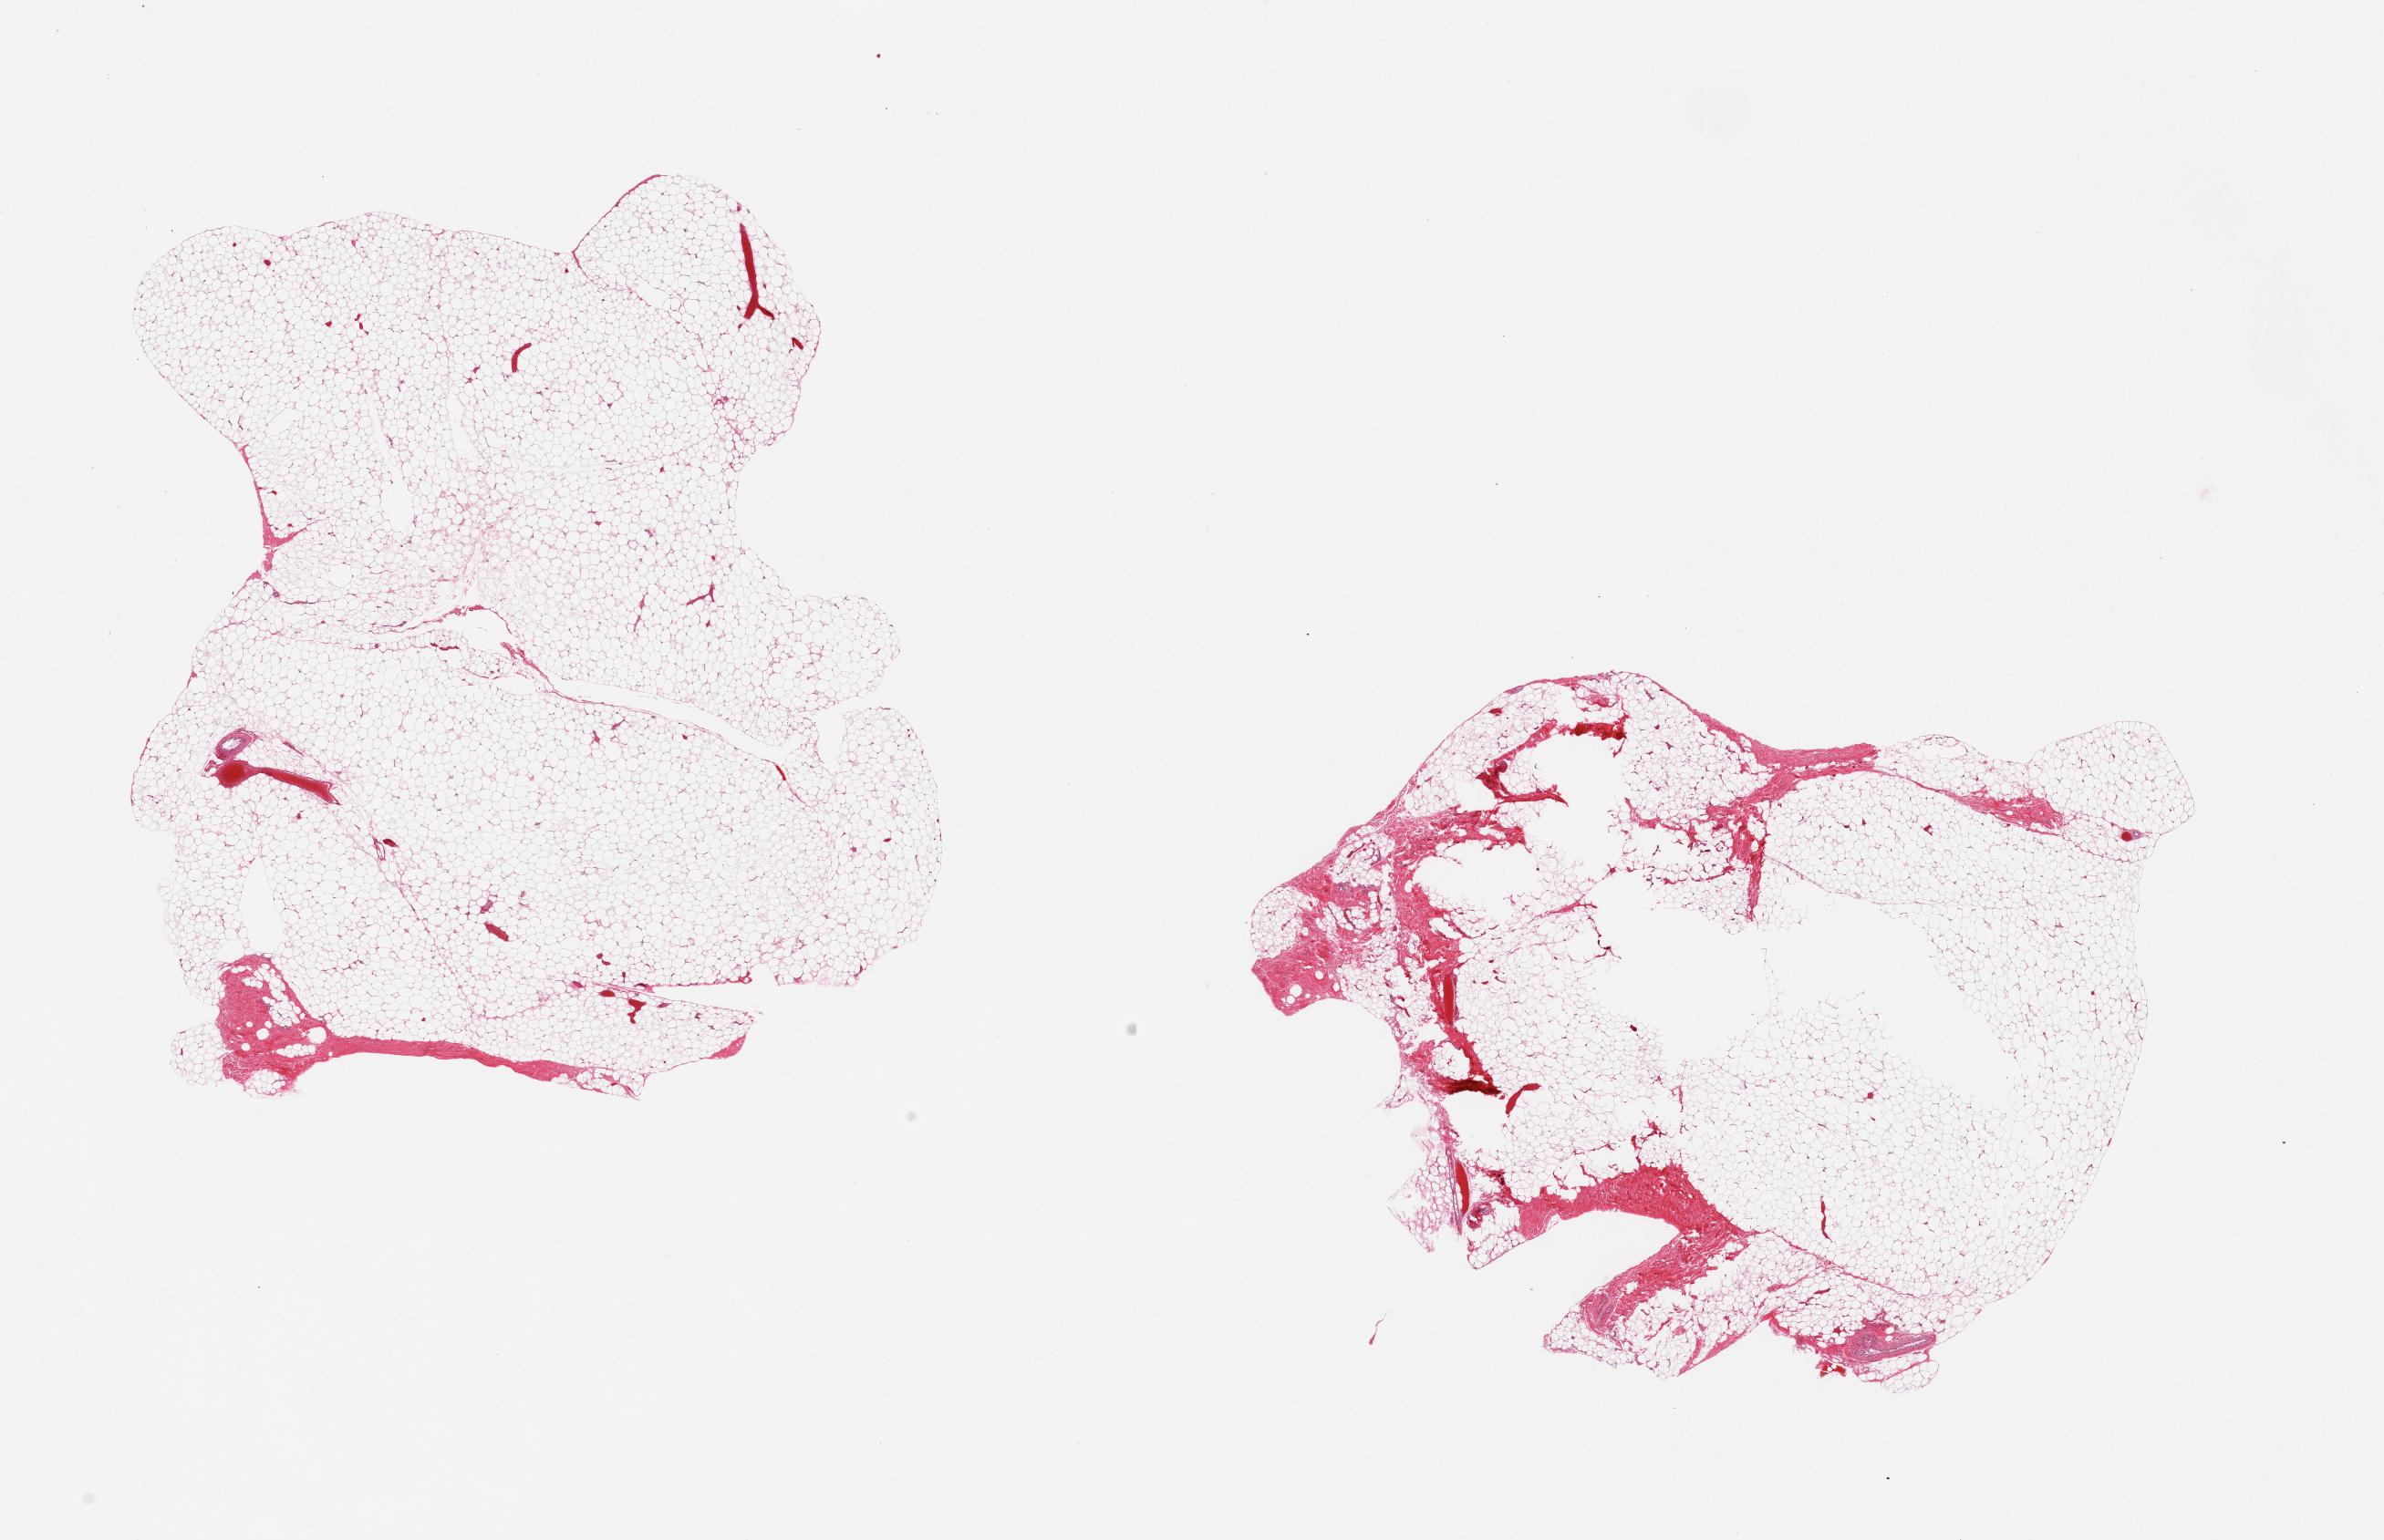
H&E whole-slide image, shown as a low-resolution overview of the whole scanned area (about 20.7 x 13.4 mm), PAXgene-fixed, paraffin-embedded tissue, sampled site (target tissue): breast, tissue donor sample. Donor: male.
Reviewer comment on this tissue sample: 2 pieces, fibroadipose elements only.